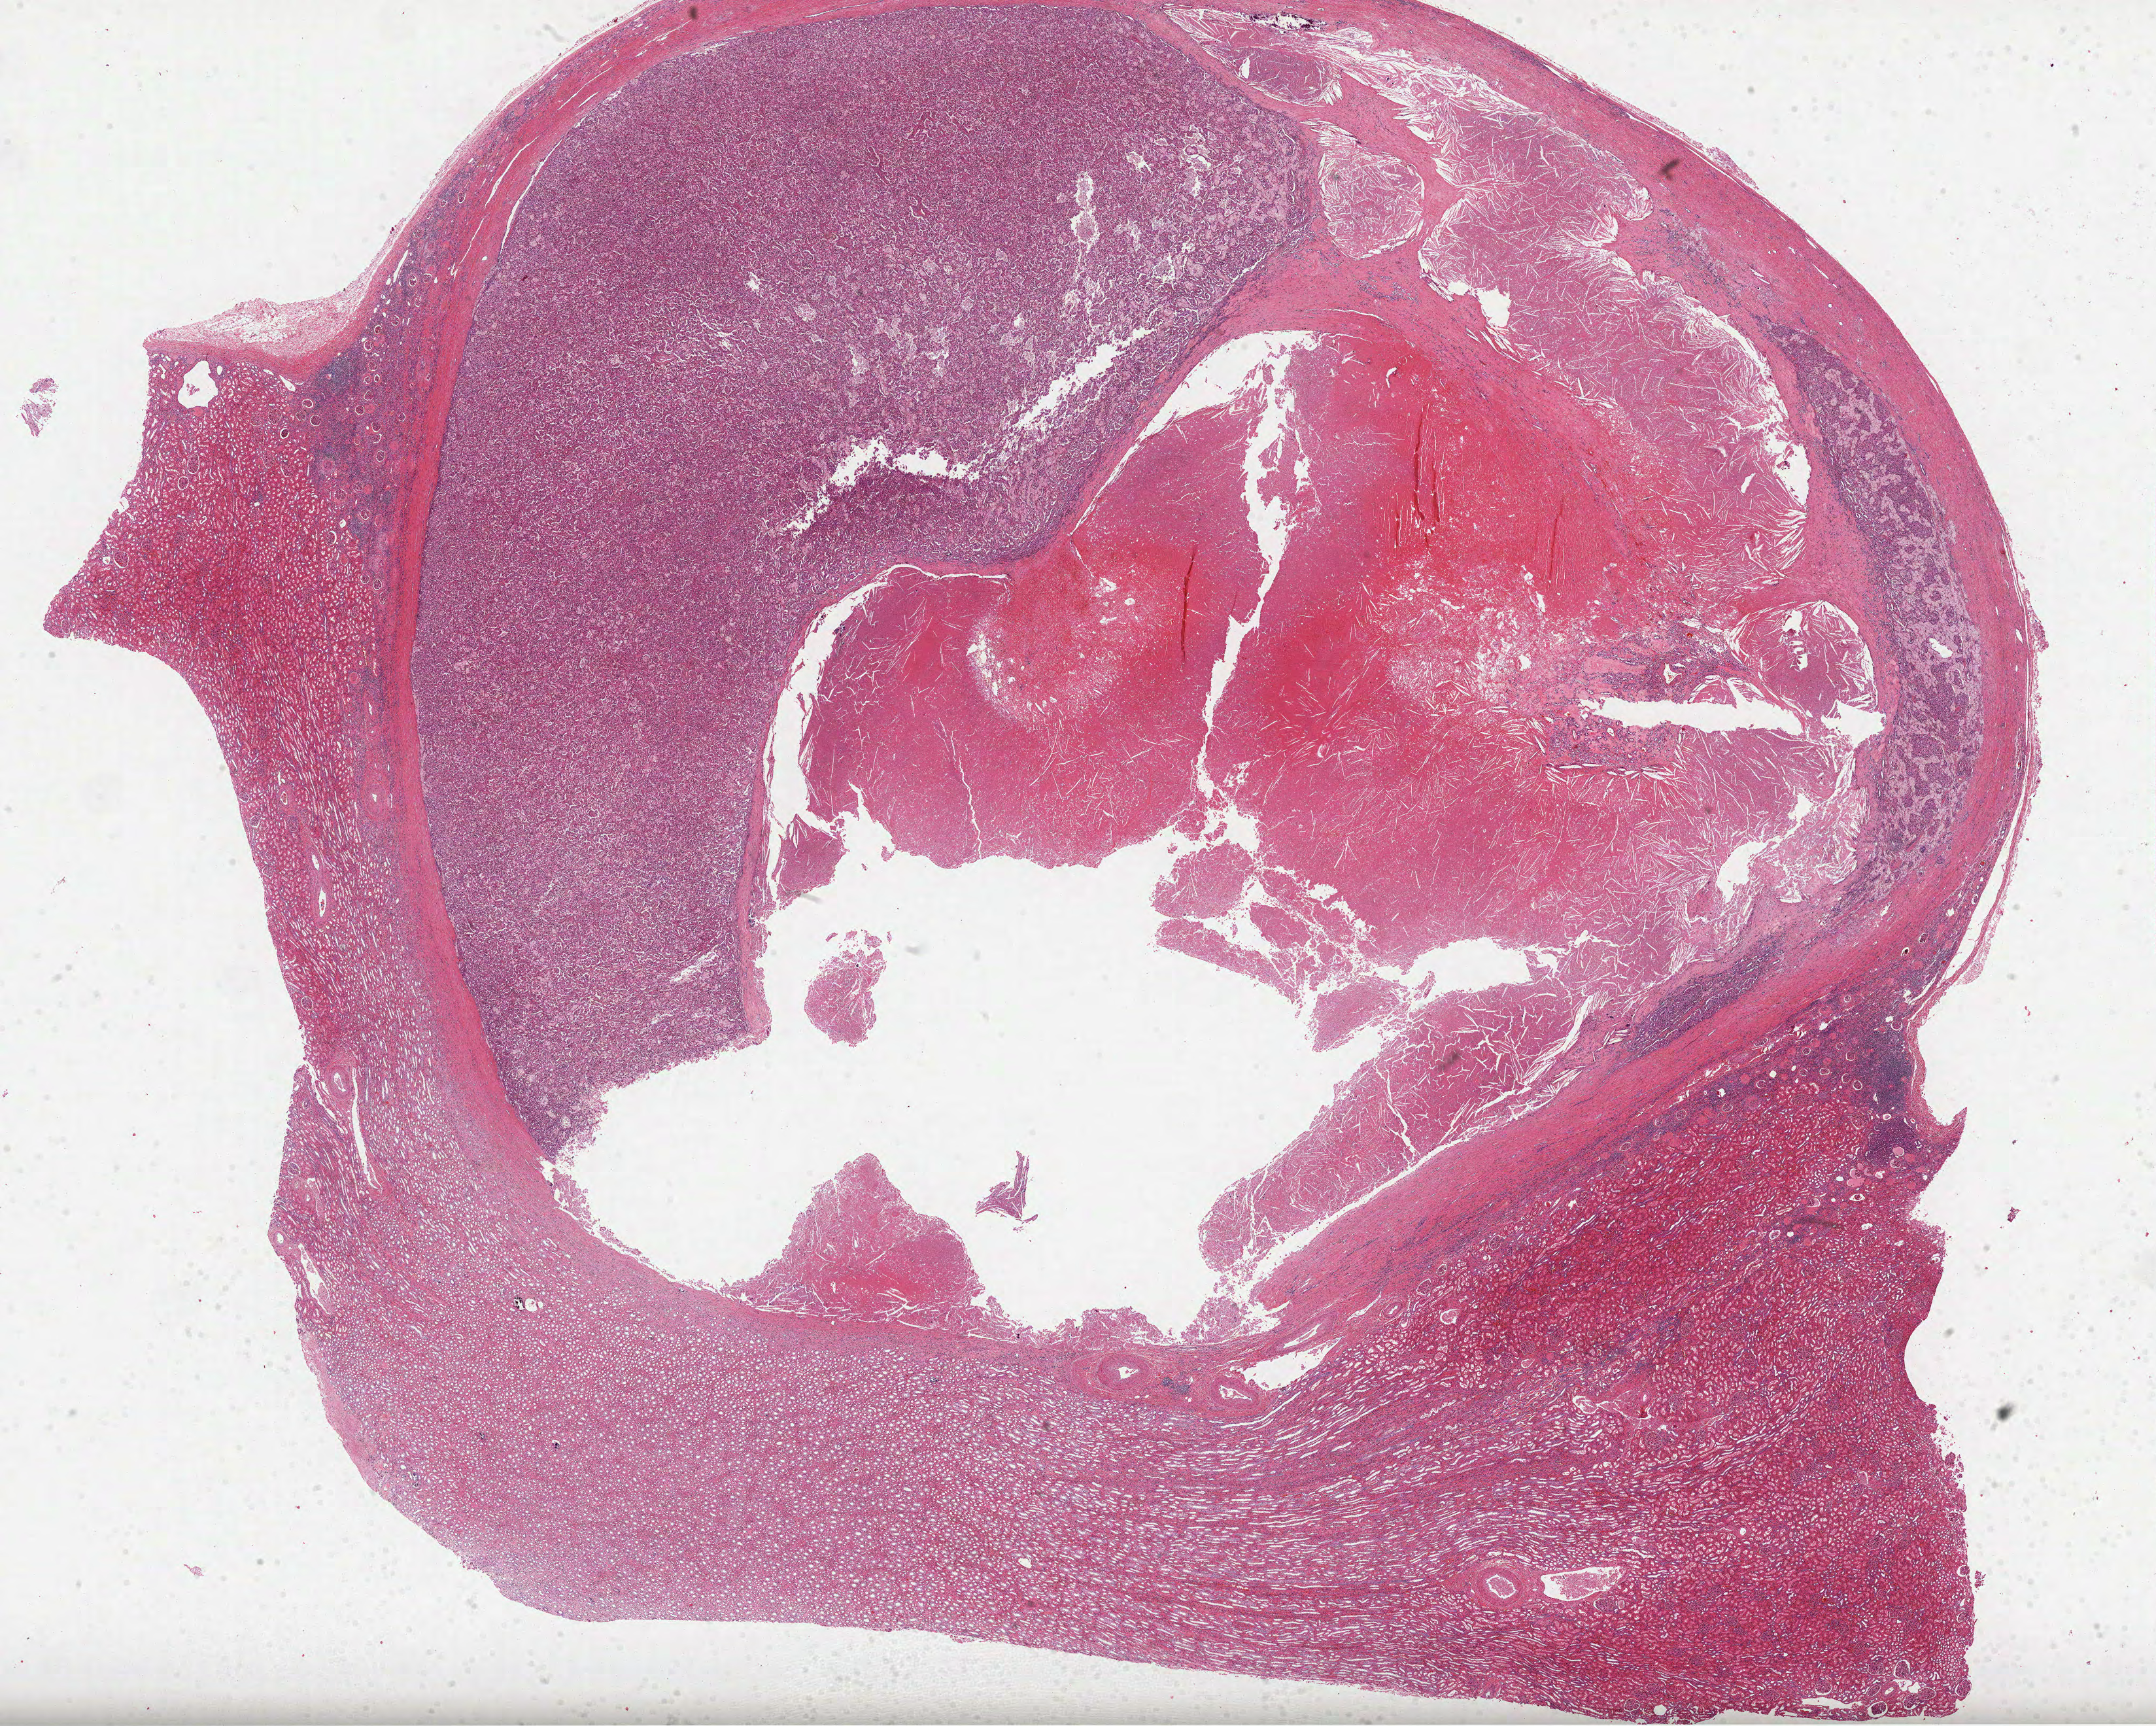
Digitized Hematoxylin and eosin (H&E) stained tissue section (whole slide), shown as a low-resolution overview of the whole scanned area (about 26.6 x 21.3 mm). Formalin-fixed paraffin-embedded (FFPE) diagnostic section. Sample: primary tumour, kidney. Female patient; age at initial diagnosis 39 years.
Histologic diagnosis: Clear cell adenocarcinoma, NOS.